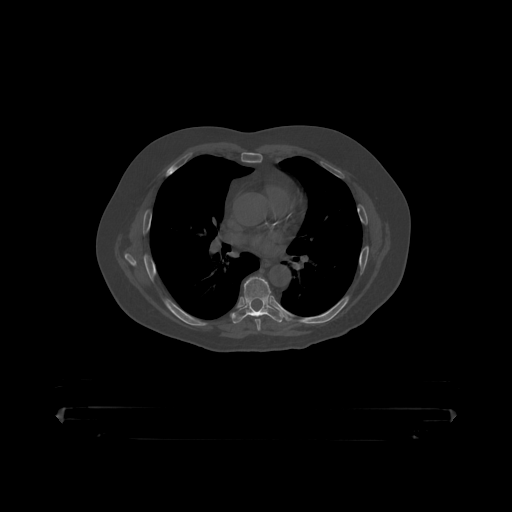
CT including the spine, one axial slice. Bone window (W 1800 / L 400 HU). 512 × 512 image matrix, field of view 650 × 650 mm. Male patient, age 60 years. Case-level facts recorded for this patient, not image findings: primary cancer: prostate.
Annotated regions visible in this slice (semi-automatically segmented with operator editing):
- T7 vertebra: bounding box <234,277,280,318> (left, top, right, bottom; pixels)